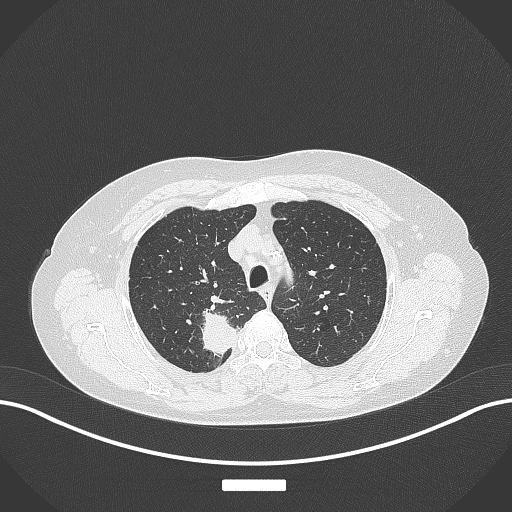
Chest CT, one axial slice; slice 302 of 357 in the series (ordered by position); reconstruction kernel B70f; lung window (W 1500 / L -600 HU); 1 mm slice thickness; 512 × 512 image matrix, field of view 400 × 400 mm. Female patient, age 62 years. From the clinical record (not read from this slice): clinical TNM (as recorded): T1c N1 M0.
Structures marked on this image (rectangle marked by the reading radiologist):
- lung tumour (recorded histology: squamous cell carcinoma): box from (x=199, y=303) to (x=238, y=358) px